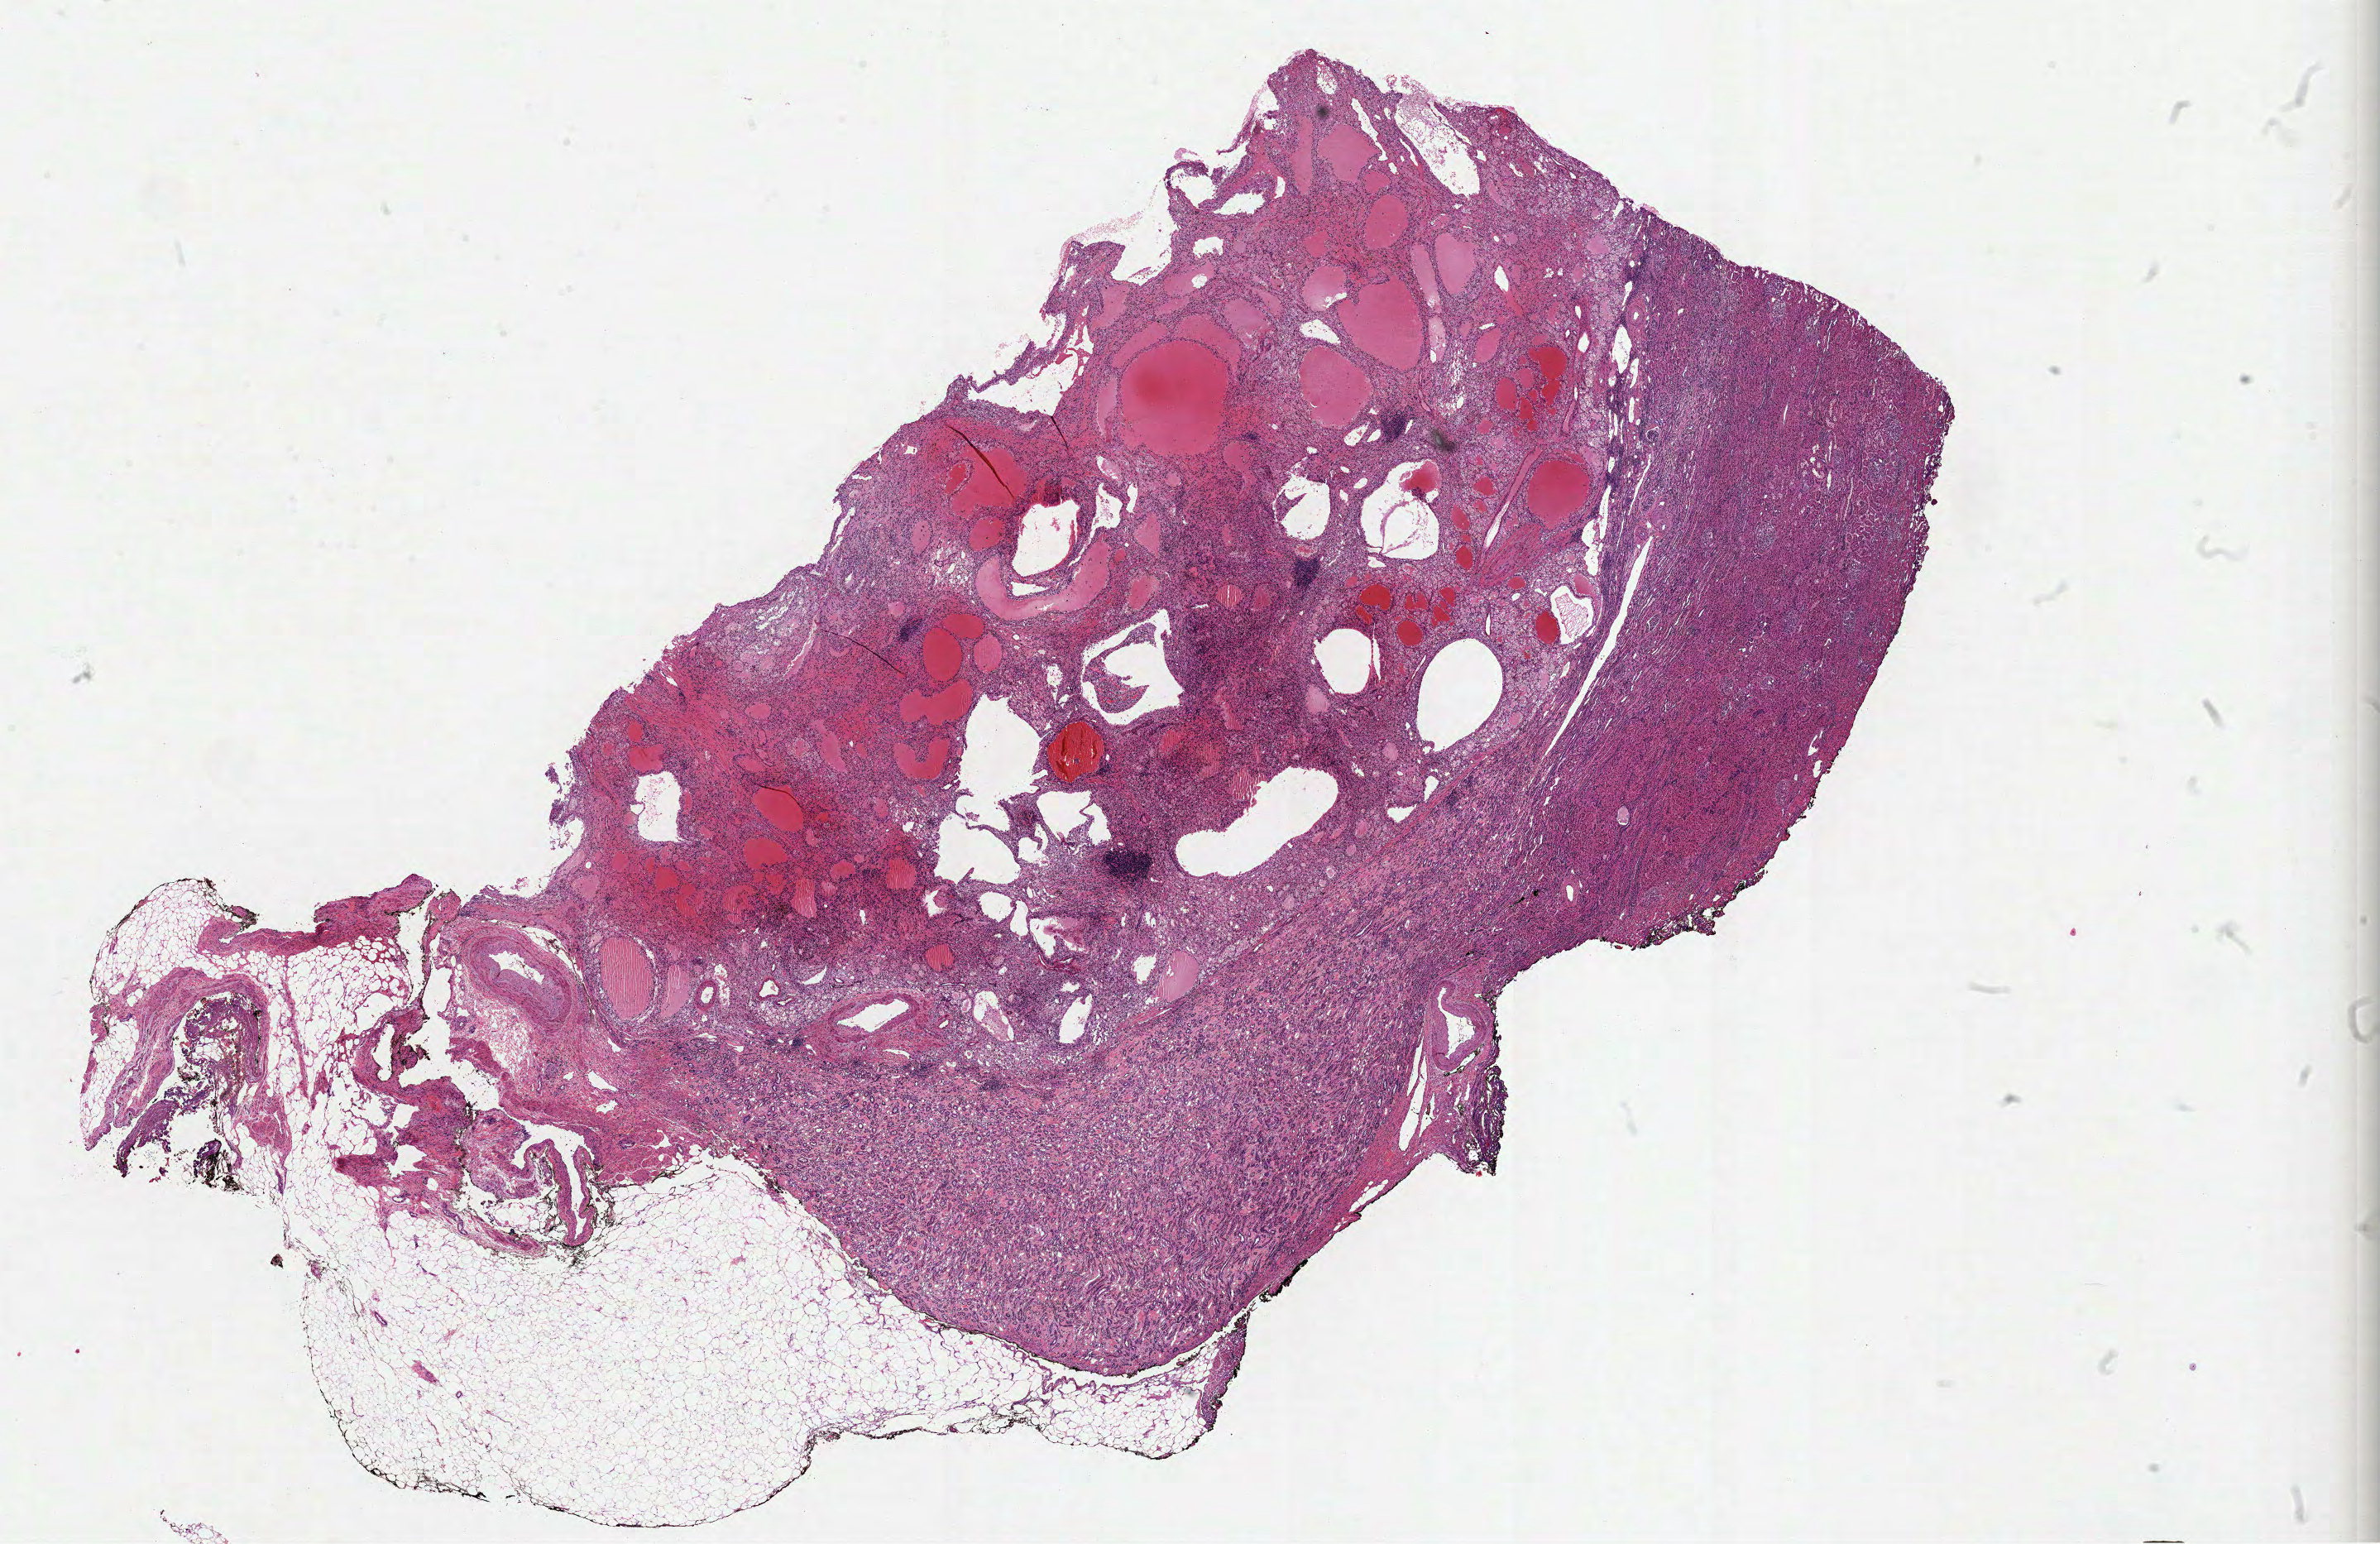
Digitized H&E-stained tissue section (whole slide), whole scanned area (about 23.2 x 15.1 mm) shown as a low-resolution overview, FFPE section, sample: primary tumour, kidney. Female, age 72 years at initial diagnosis.
Pathologic diagnosis: Clear cell adenocarcinoma, NOS.